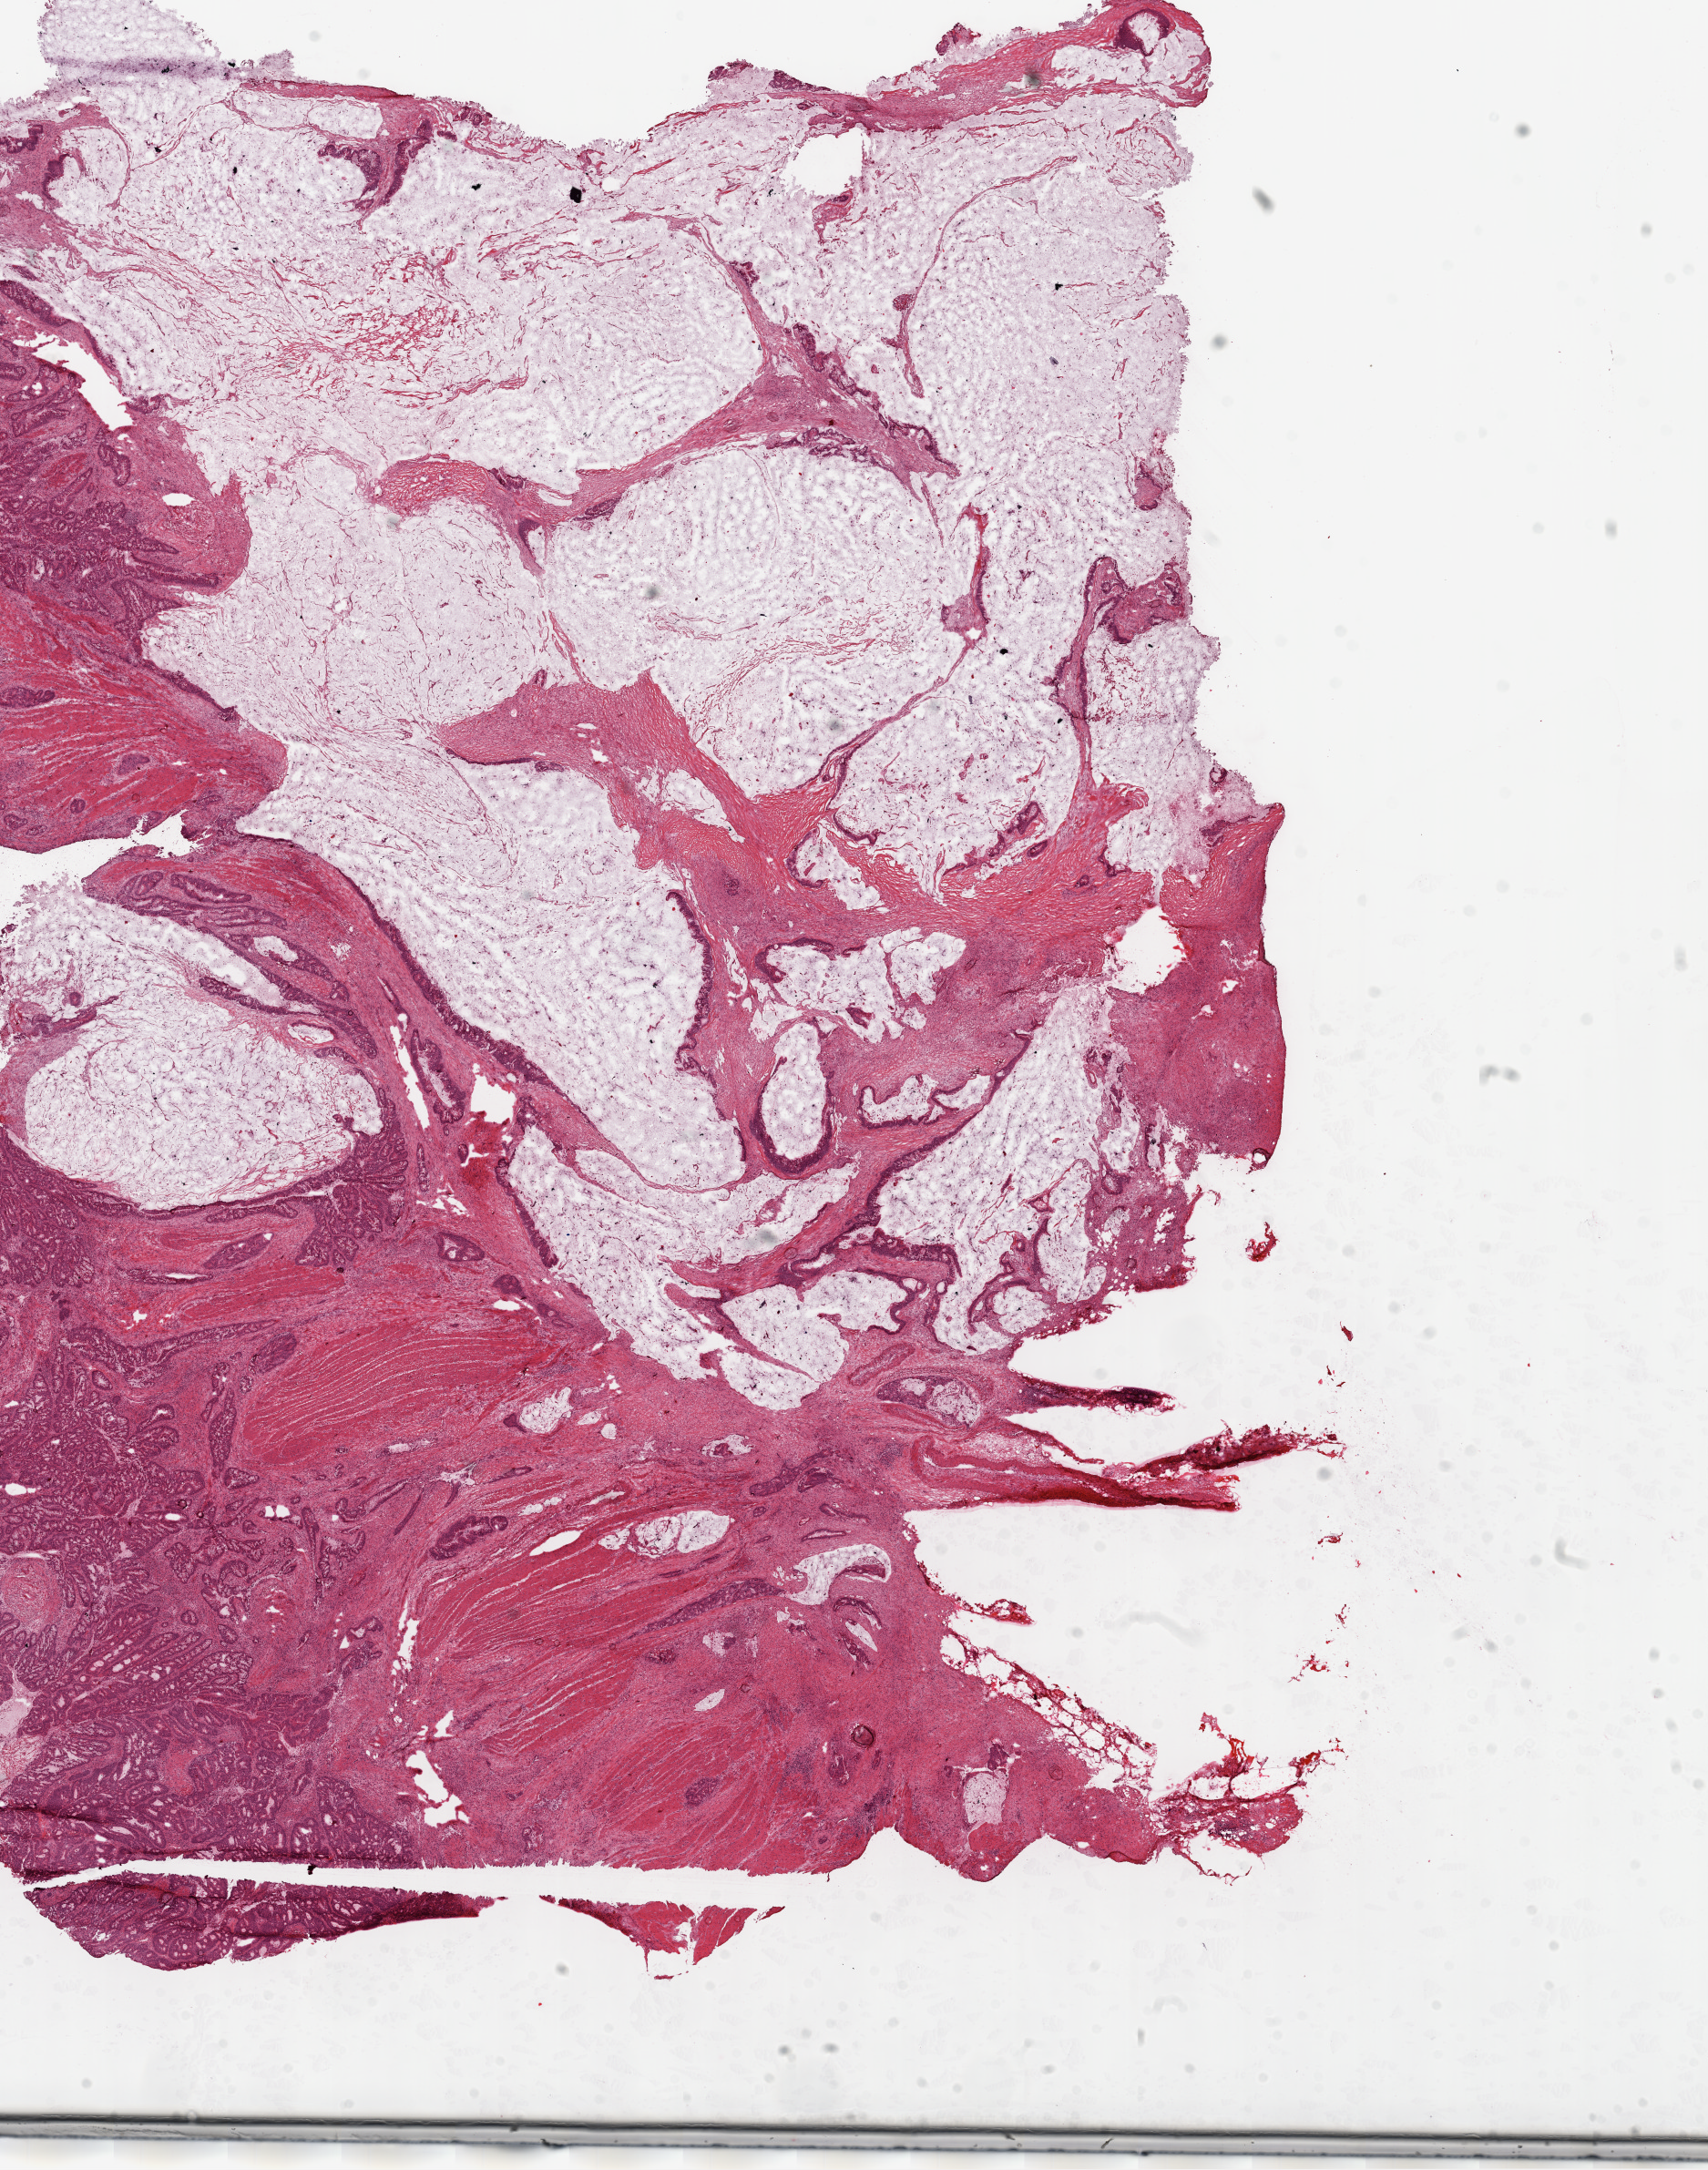
Digitized Hematoxylin and eosin (H&E) stained tissue section (whole slide), a low-resolution overview of the entire scanned area, about 15.0 x 19.1 mm. Frozen section from the top of the tissue portion. Colon, primary tumour sample. Male patient; age at initial diagnosis 53 years. Slide review estimates, as recorded: tumour cells 83%, tumour nuclei 75%, normal cells 0%, stromal cells 15%, necrosis 2%.
- pathologic diagnosis: Mucinous adenocarcinoma (transverse colon)
- lymph nodes positive (case pathology): 1 of 23 examined
- AJCC pathologic stage: IIIB